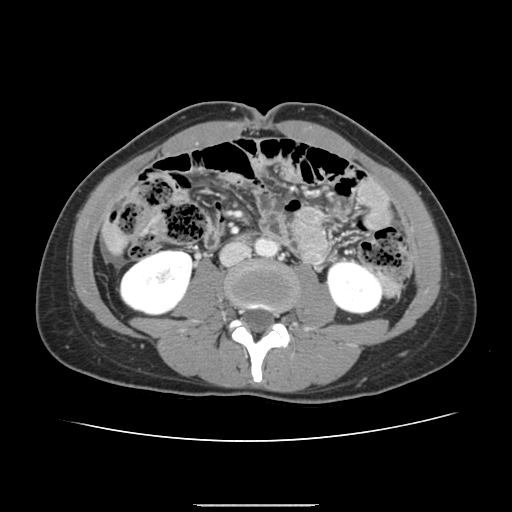
Contrast-enhanced abdominal CT, one axial slice. Position 34 of 150 along the scan axis. 120 kVp. Intravenous contrast given. Soft-tissue window (W 400 / L 40 HU). 2.5 mm slice thickness. 512 × 512 image matrix. Female patient, age 32 years. From the clinical record (not read from this slice): diagnosis: colorectal cancer liver metastases, imaged before liver resection; multiple liver metastases: yes; largest metastasis: 0.7 cm.
Annotated regions visible in this slice (expert manual segmentation):
- liver: bounding box <110,232,122,248> (left, top, right, bottom; pixels)
- planned liver remnant (the part of the liver to remain after resection): <110,233,121,249>